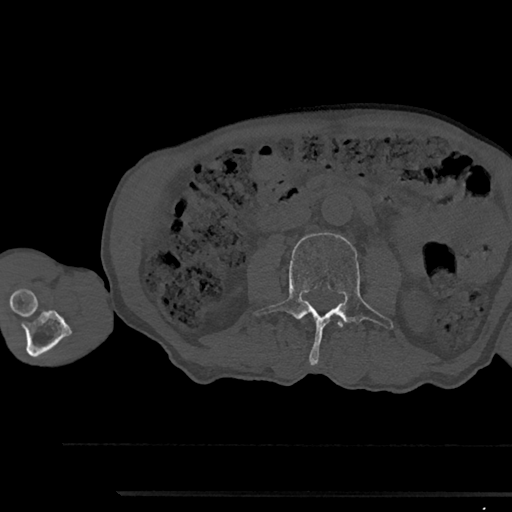
CT including the spine, one axial slice. Position 497 of 797 along the scan axis. 120 kVp. Bone window (W 1800 / L 400 HU). 0.5 mm slice thickness. 512 × 512 image matrix, field of view 367 × 367 mm. Male patient, age 79 years. From the clinical record (not read from this slice): primary cancer: prostate.
Annotated regions visible in this slice (semi-automatic segmentation, software-assisted and operator-edited):
- L2 vertebra: box from (x=338, y=320) to (x=342, y=327) px
- L3 vertebra: (x=253, y=233)–(x=393, y=365)